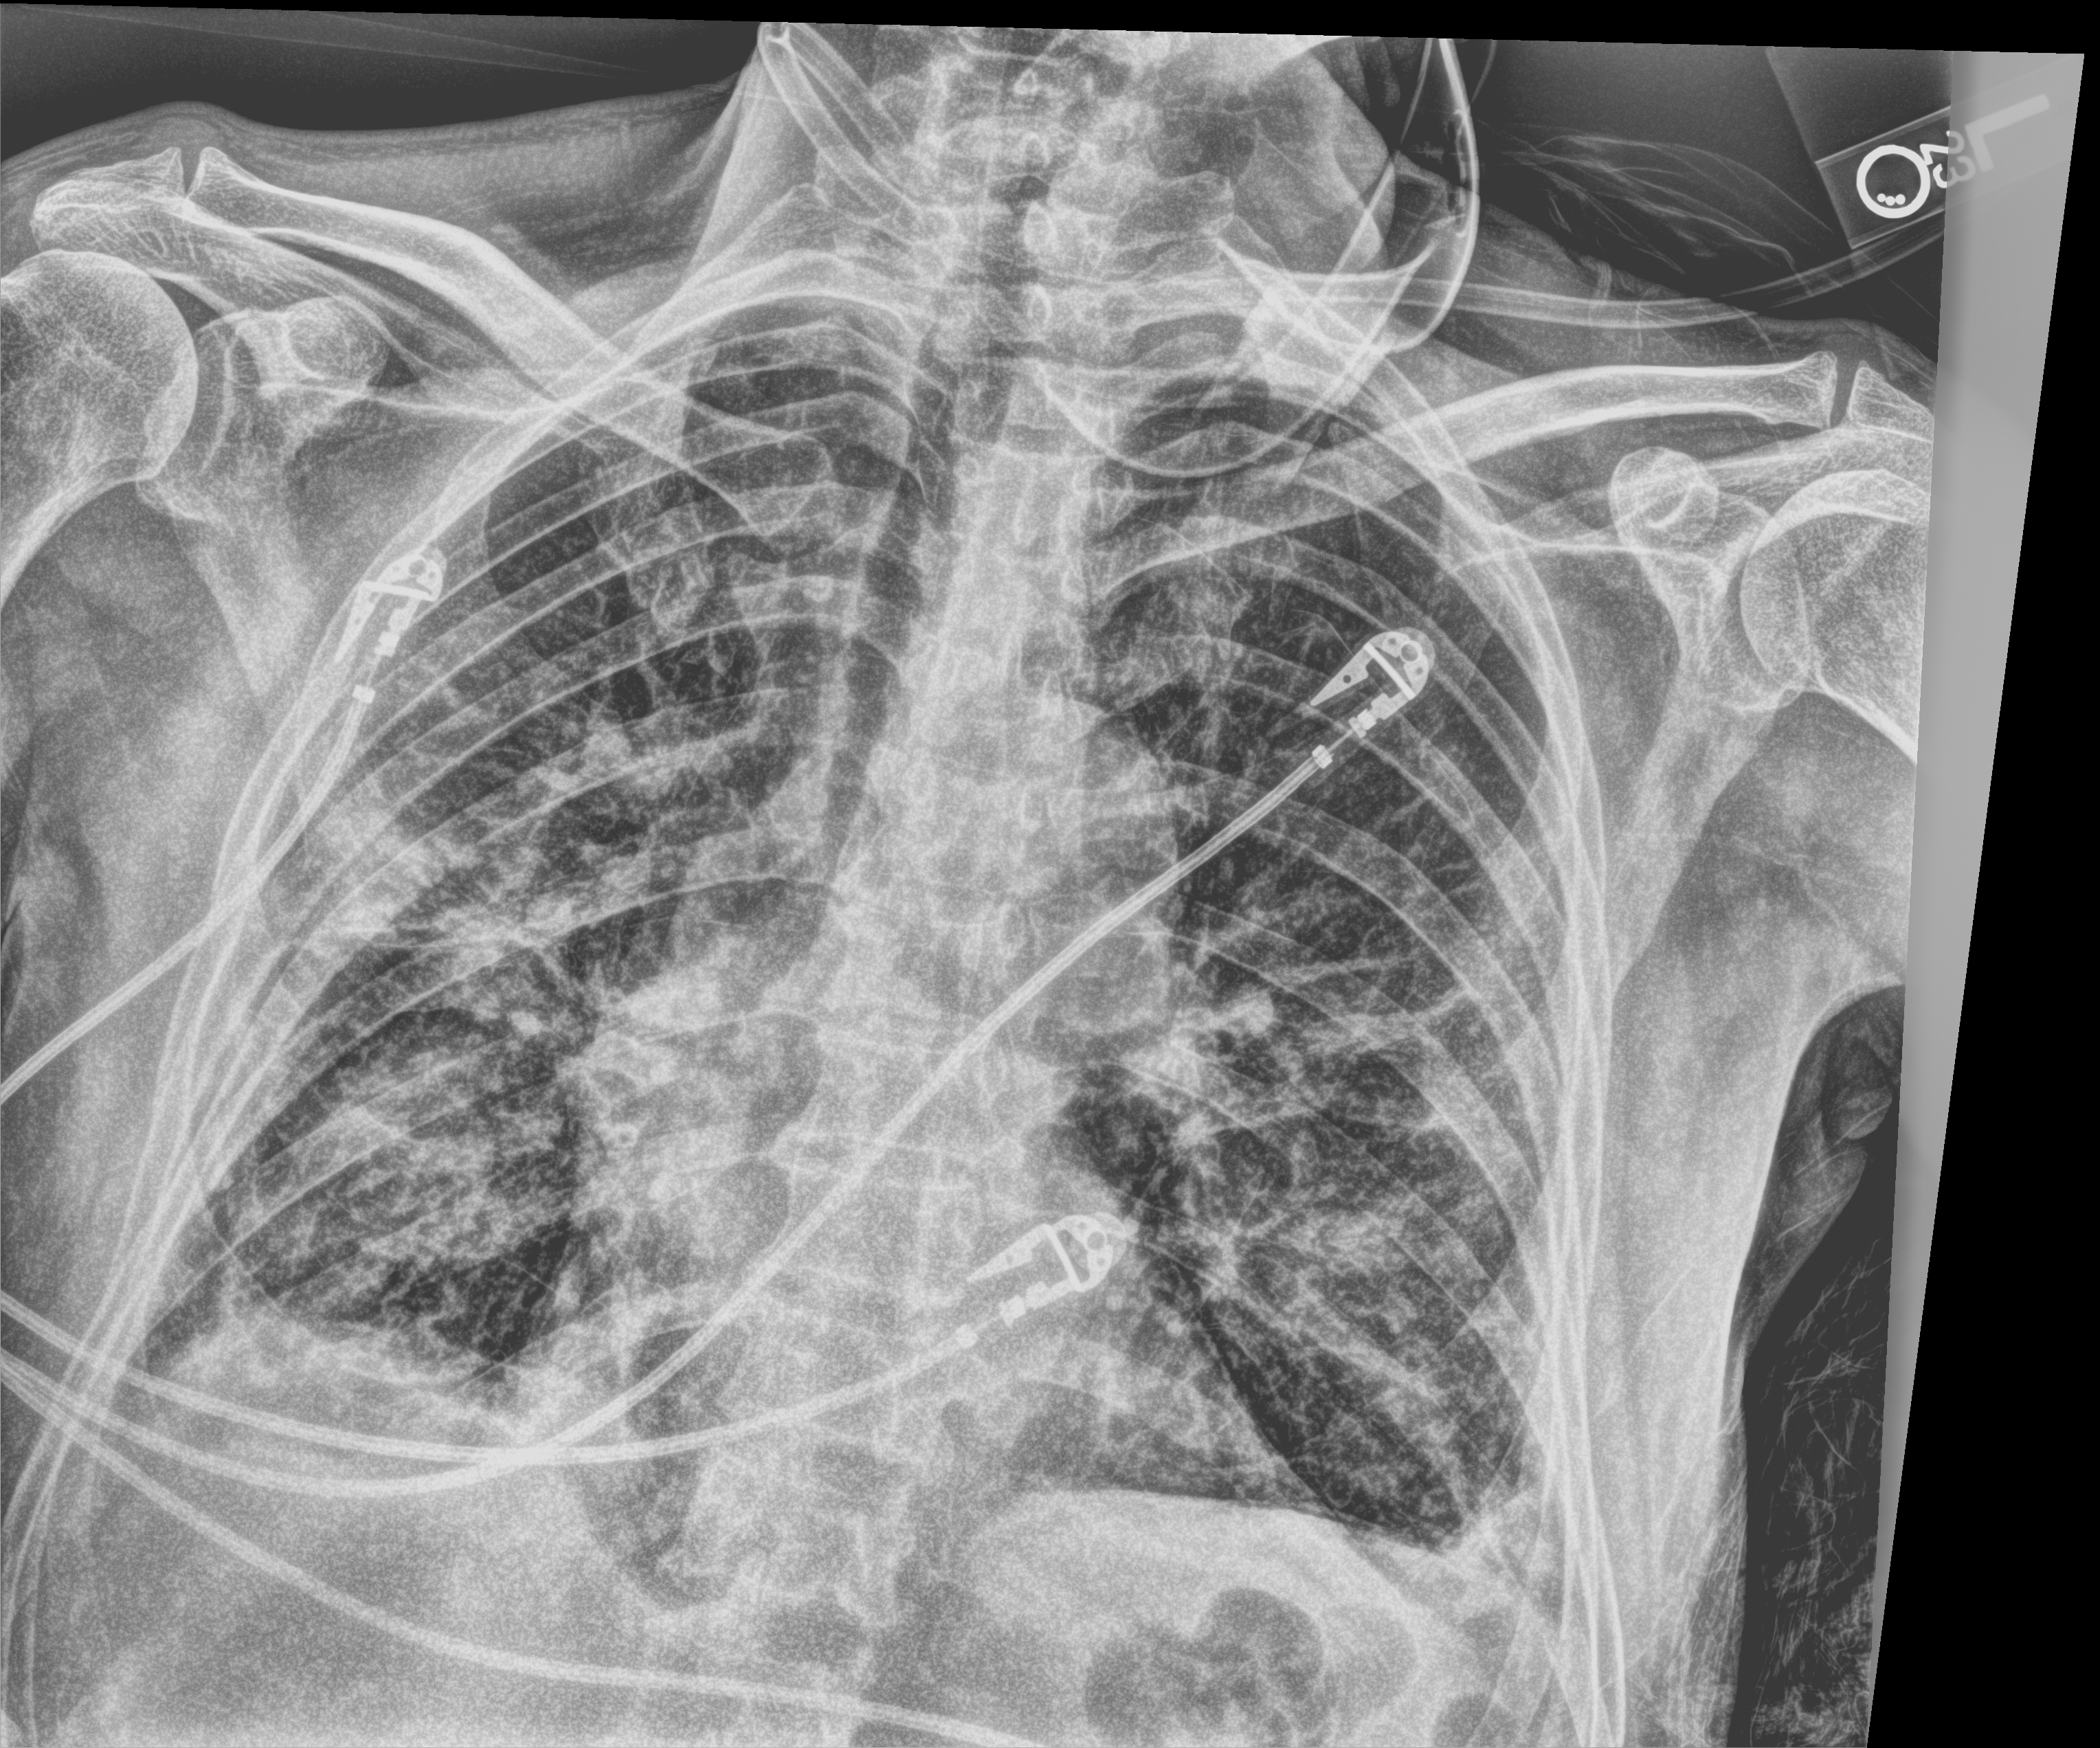
Bedside chest radiograph (computed radiography); anteroposterior (AP) projection. Male patient hospitalised with COVID-19, age 75–90 years.
Hospital-stay facts (about this admission, not read from this image; timing relative to this image not recorded): other chronic lung disease (admission record): yes; length of hospital stay: 70 days; mechanically ventilated during this hospital stay: yes.